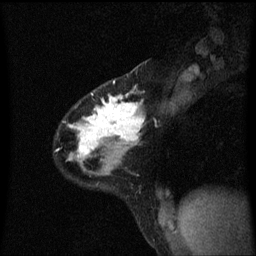
Breast MRI (dynamic contrast-enhanced), one sagittal slice. Slice 42 of 60 in the series (ordered by position). Dynamic contrast-enhanced series, image 2 of 3 at this slice position (ordered by acquisition). 1.5 T. TE 4.2 ms, TR 8.4 ms. 256 × 256 image matrix, field of view 200 × 200 mm. Female patient, age 32 years.
Outlined on this slice (semi-automatically segmented with operator editing):
- analysis volume of interest (the breast-tissue region the enhancement analysis was run in; not a lesion): box from (x=58, y=80) to (x=146, y=169) px
- tumour enhancement mask (voxels above the 70 % enhancement threshold inside the analysis volume of interest): (x=70, y=94)–(x=145, y=161)